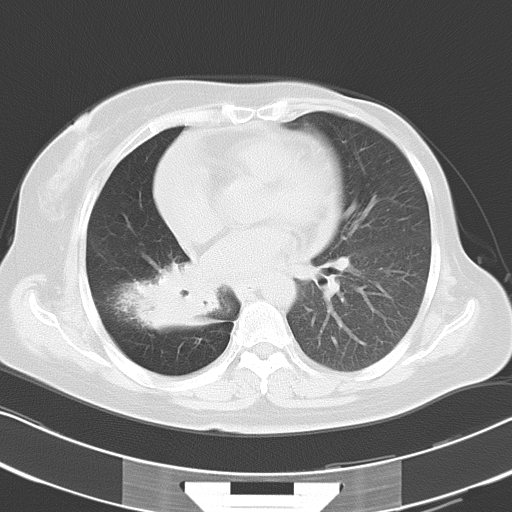
Chest CT, one axial slice. Slice 15 of 30 in the series (ordered by position). Reconstruction kernel B70f. 120 kVp. Lung window (W 1500 / L -600 HU). 8 mm slice thickness. 512 × 512 image matrix. Female patient, age 53 years. From the clinical record (not read from this slice): clinical TNM (as recorded): T2b N1 M0.
Annotated regions visible in this slice (bounding box drawn by a radiologist):
- lung tumour (recorded histology: adenocarcinoma): bounding box (x1, y1, x2, y2) in pixels: (109, 254, 229, 337)